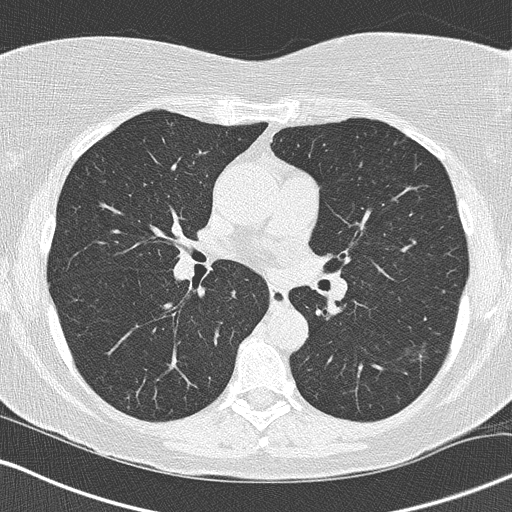
Low-dose screening chest CT, axial slice. Third annual screen. Lung window (W 1500 / L -600 HU). 2 mm slice thickness. Lung (sharp) reconstruction kernel (B50f). Female participant, aged 57 years at enrolment. Current smoker at enrolment.
Lesion marked by an expert reader, bounding box [x1, y1, x2, y2] px = [389, 325, 460, 383]. The screening reader recorded 5 non-calcified nodules or masses ≥4 mm on this exam (left lower lobe, right upper lobe, right lower lobe, right upper lobe); which of them this box marks is not recorded. Later outcome: lung cancer diagnosed 51 days after this screen — bronchiolo-alveolar adenocarcinoma, NOS, left lower lobe, well differentiated (G1), stage IA (AJCC 6th edition), 16 mm at pathology.